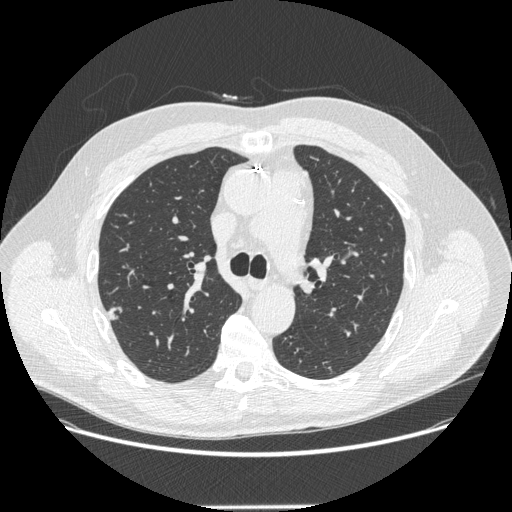
Chest CT (low-dose screening protocol), one axial image. Third annual screen. Lung window (W 1500 / L -600 HU). 1.25 mm slice thickness. Male participant, aged 62 years at enrolment. Current smoker at enrolment.
Expert-annotated lung lesion, bounding box (x1, y1, x2, y2) in pixels: (94, 298, 133, 333). Screening reader's record for this exam (one nodule recorded; not confirmed to be the boxed lesion): non-calcified nodule or mass ≥4 mm, right upper lobe, 12 × 11 mm, smooth margins, soft tissue attenuation, pre-existing on the prior screen: yes; interval growth: yes. Participant outcome: lung cancer diagnosed 112 days after this screen — adenocarcinoma, NOS, right upper lobe, moderately differentiated (G2), stage IA (AJCC 6th edition), 12 mm at pathology.